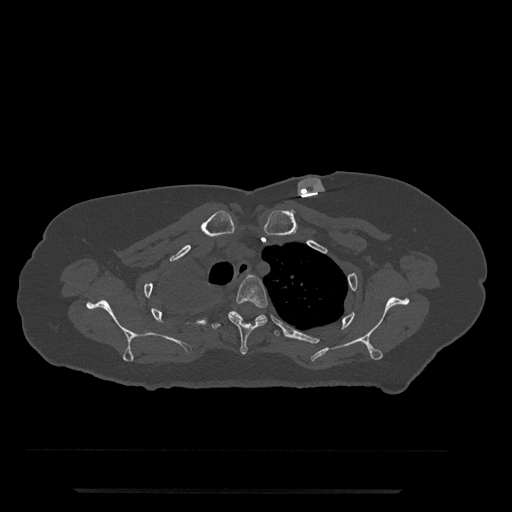
CT including the spine, one axial slice; position 621 of 797 along the scan axis; reconstruction kernel Br40s/3; 120 kVp; bone window (W 1800 / L 400 HU); 0.5 mm slice thickness; 512 × 512 image matrix, field of view 440 × 440 mm. Female patient, age 51 years. From the clinical record (not read from this slice): primary cancer: neuro.
Annotated regions visible in this slice (semi-automatic segmentation, software-assisted and operator-edited):
- T3 vertebra: bounding box <228,275,268,355> (left, top, right, bottom; pixels)
- T4 vertebra: <211,310,286,337>